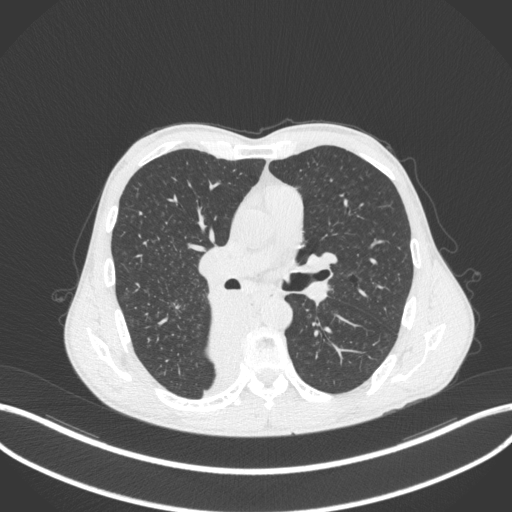
Chest CT, one axial slice; position 218 of 371 along the scan axis; reconstruction kernel B31f; lung window (W 1500 / L -600 HU); 1 mm slice thickness; 512 × 512 image matrix. Male patient, age 58 years. Case-level facts recorded for this patient, not image findings: clinical TNM (as recorded): T3 N1 M1.
Outlined on this slice (bounding box drawn by a radiologist):
- lung tumour (recorded histology: squamous cell carcinoma): bounding box (x1, y1, x2, y2) in pixels: (206, 290, 254, 379)